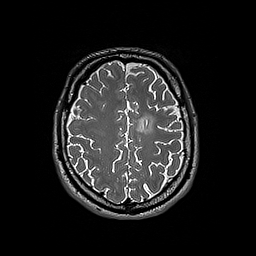
Brain MRI from a brain-tumour surgery series, one axial slice. 1 mm slice thickness. 256 × 256 image matrix, field of view 250 × 250 mm. Case-level facts recorded for this patient, not image findings: histopathology: Oligodendroglioma; WHO grade: 3; IDH mutation: yes; tumour location: Left Frontal.
Structures marked on this image (outlined manually by an expert reader):
- tumour: bounding box (x1, y1, x2, y2) in pixels: (136, 115, 156, 134)